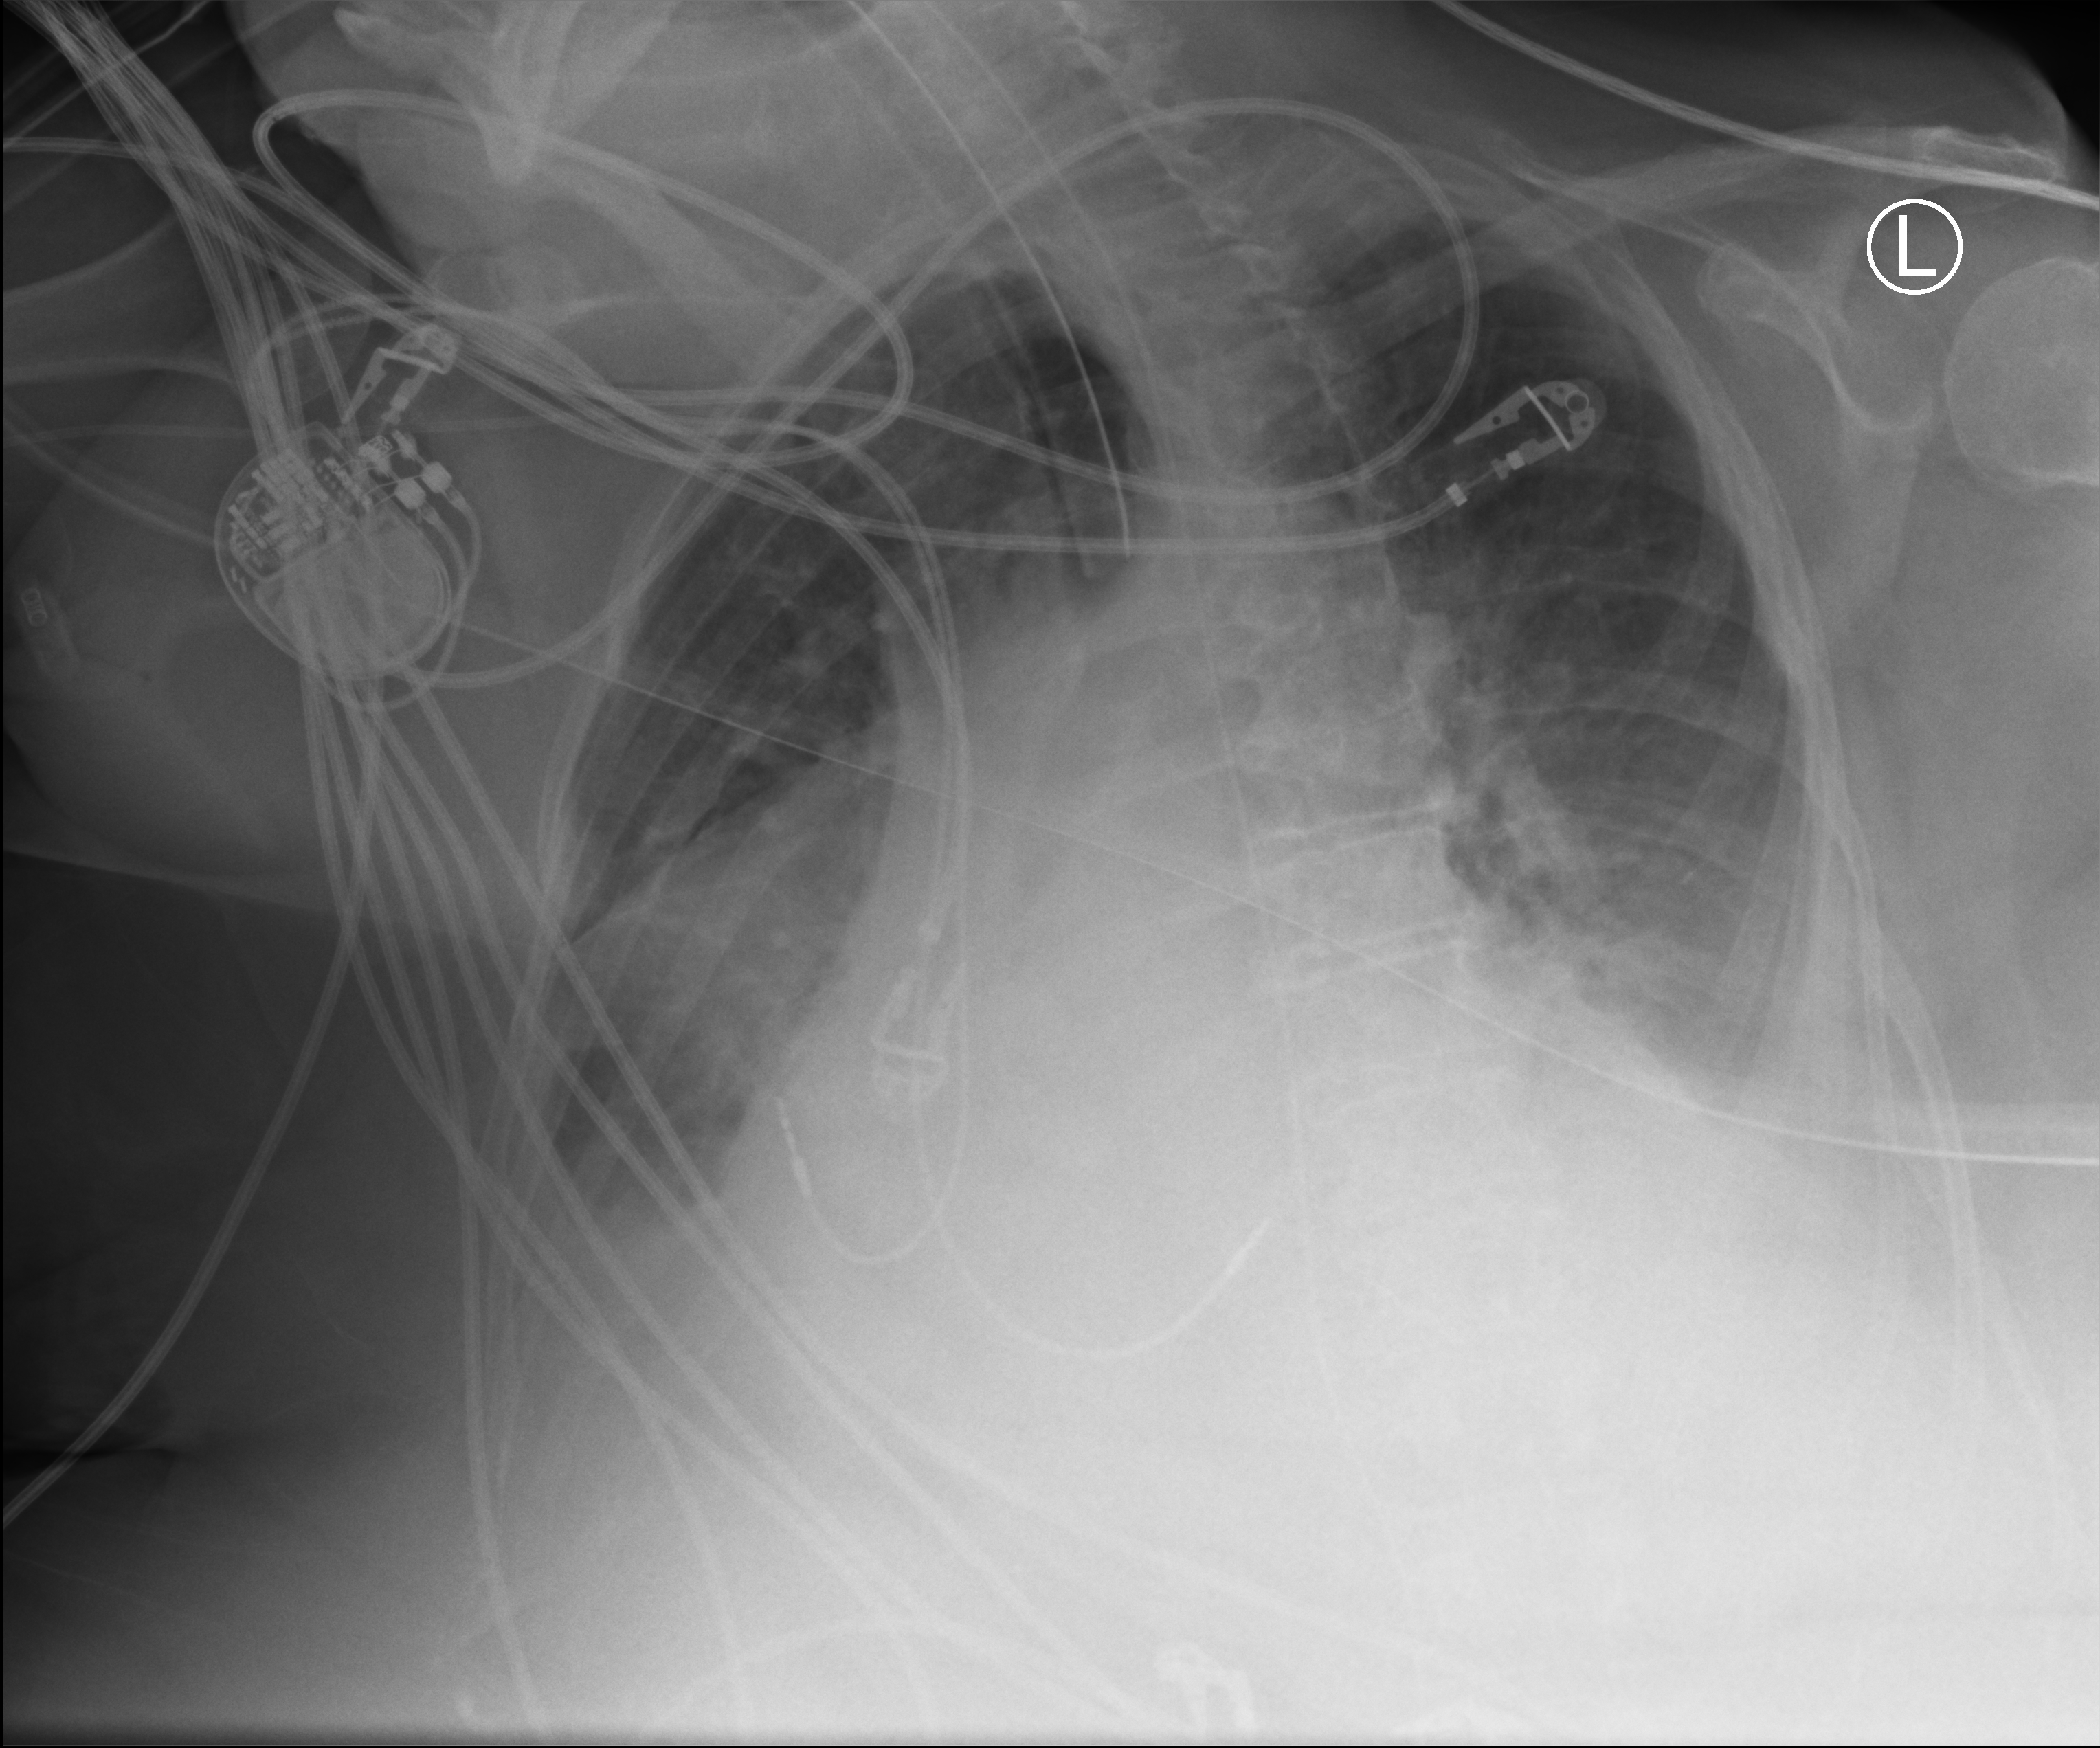
Chest X-ray (portable); anteroposterior (AP) projection. Patient hospitalised with COVID-19; female, aged 75–90 years.
Admission-level facts for this patient (not findings on this image; timing relative to this image not recorded):
- mechanically ventilated during this hospital stay: yes